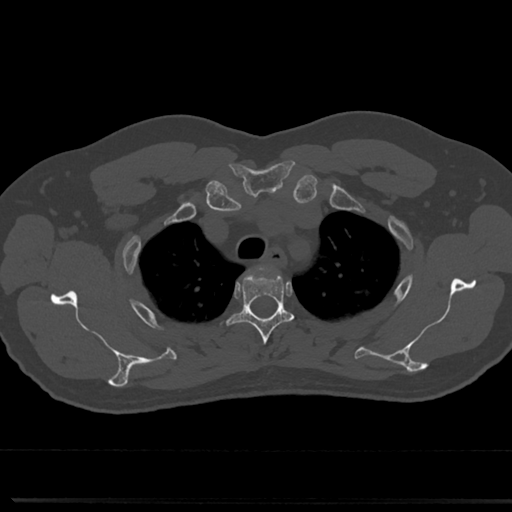
CT including the spine, one axial slice; position 593 of 817 along the scan axis; 120 kVp; bone window (W 1800 / L 400 HU); 0.5 mm slice thickness; 512 × 512 image matrix, field of view 355 × 355 mm. Male patient, age 61 years. From the clinical record (not read from this slice): primary cancer: prostate.
Annotated regions visible in this slice (semi-automatically segmented with operator editing):
- T3 vertebra: bounding box <233,266,292,349> (left, top, right, bottom; pixels)